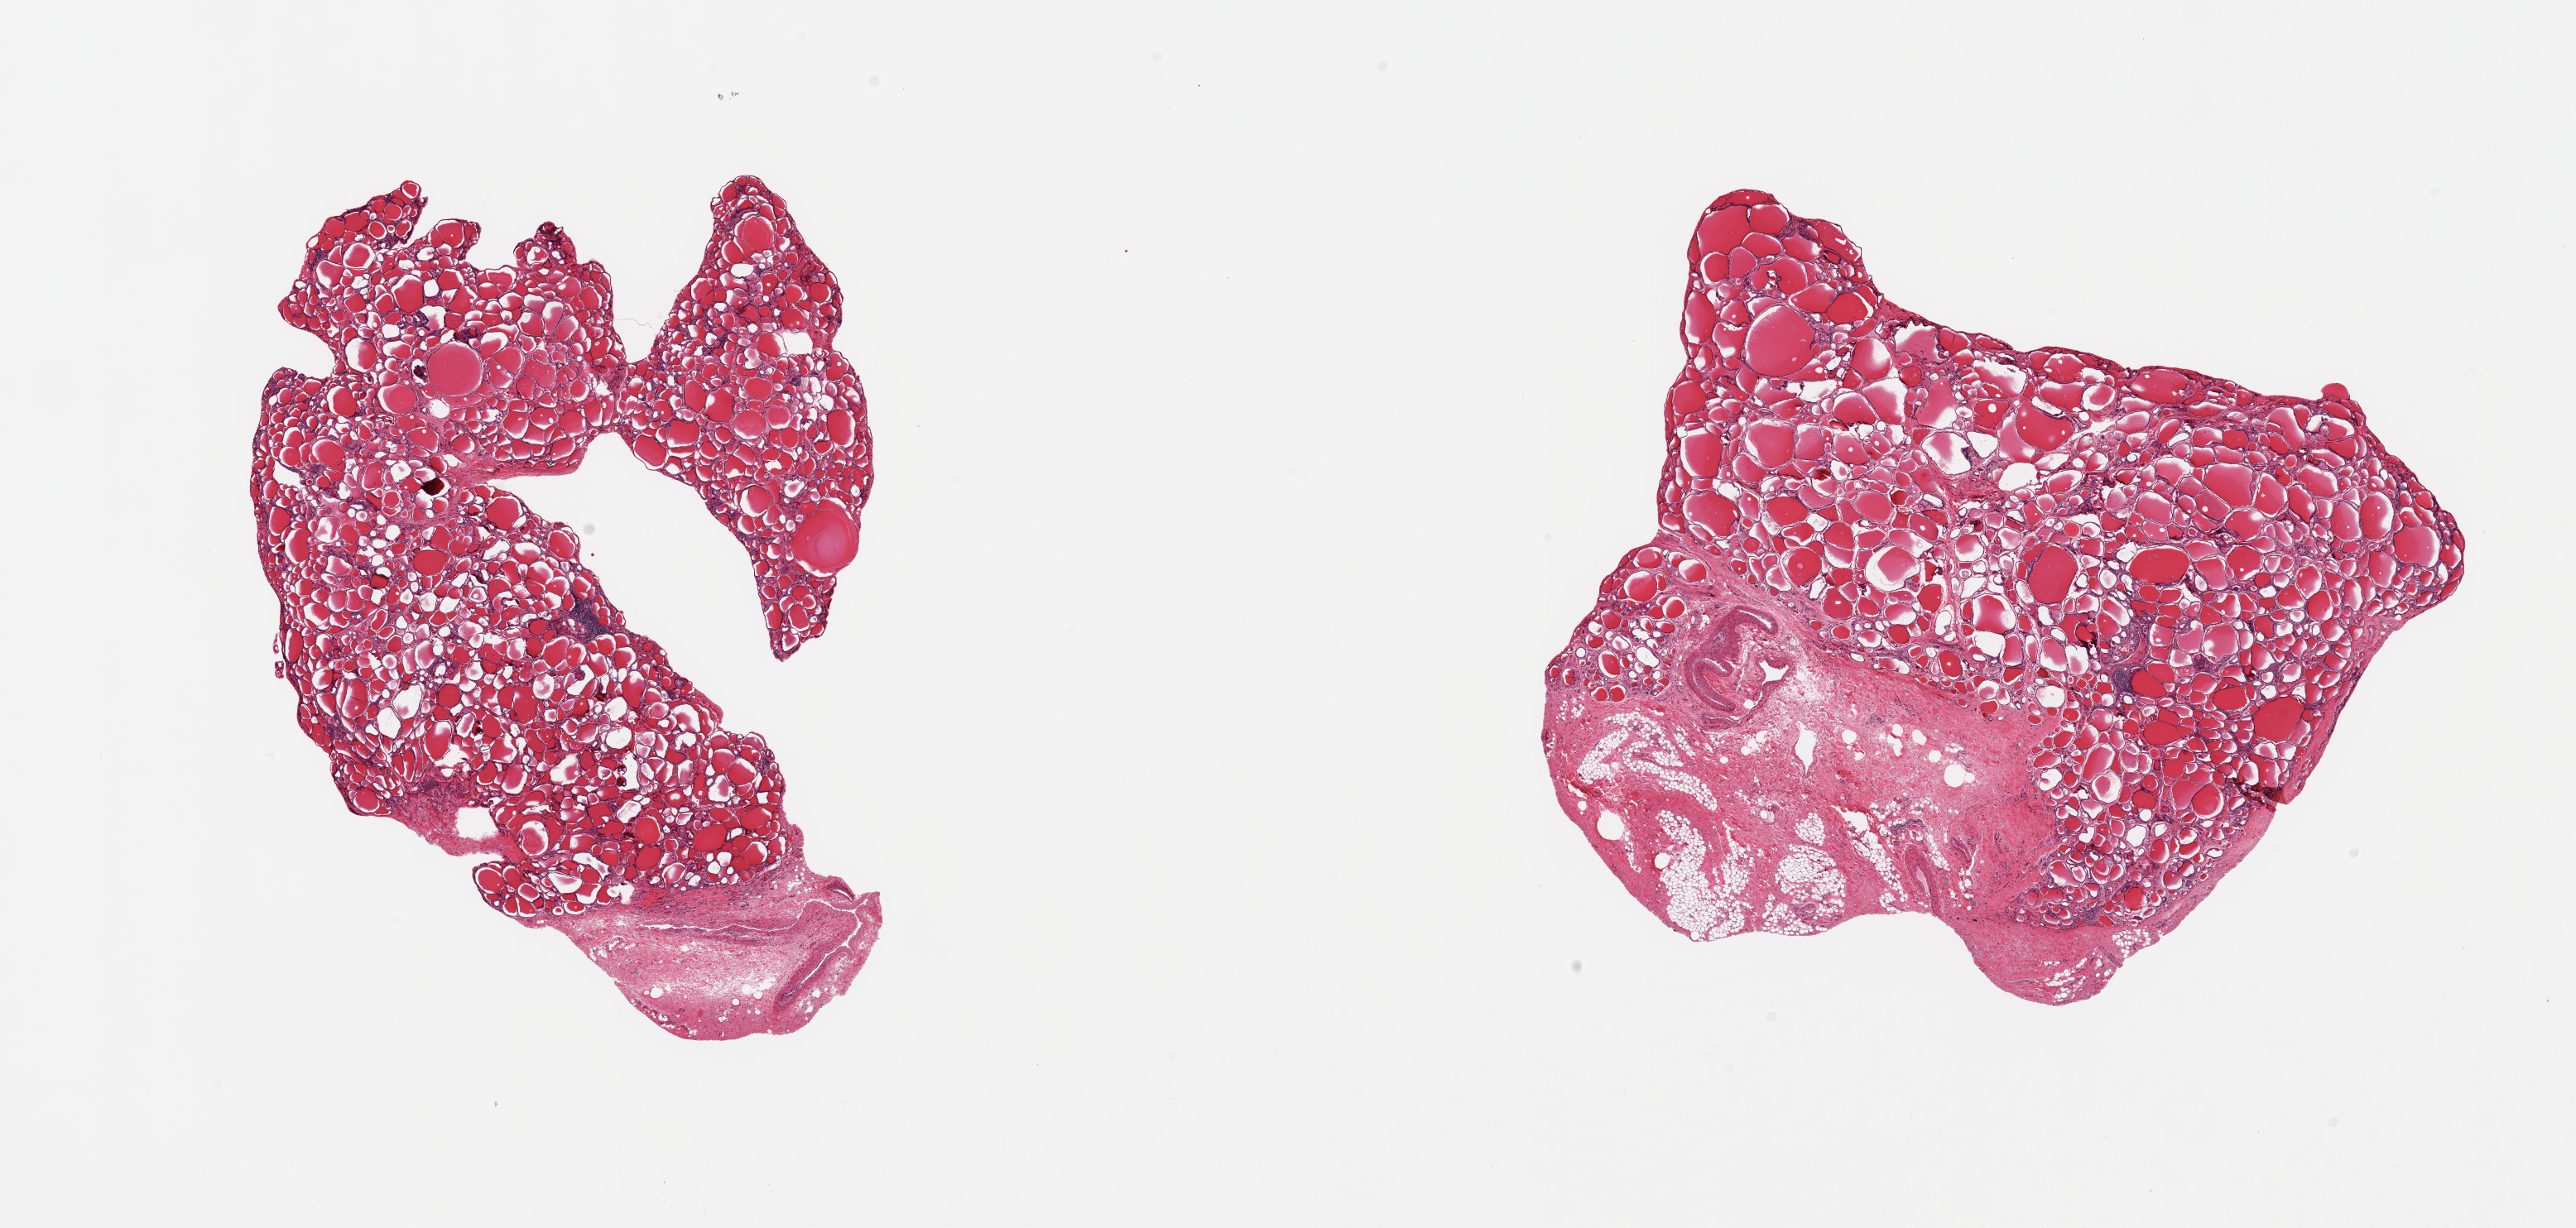
Digitized haematoxylin and eosin-stained section, whole scanned area (about 24.6 x 11.7 mm, slide scanned at 20x) shown as a low-resolution overview, PAXgene-fixed, paraffin-embedded tissue, section of thyroid (target tissue), tissue donor sample. Male donor.
• reviewer comment on this tissue sample: 2 pieces; 30% & 20% external fibromuscular stroma